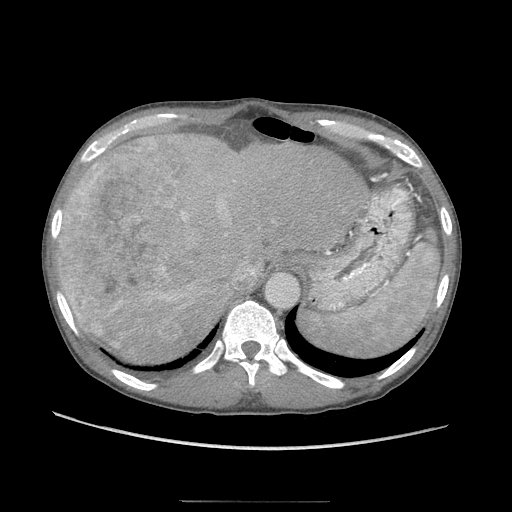
Contrast-enhanced abdominal CT (liver protocol), one axial slice; position 73 of 103 along the scan axis; reconstruction kernel STANDARD; 120 kVp; soft-tissue window (W 400 / L 40 HU); 2.5 mm slice thickness; 512 × 512 image matrix, field of view 380 × 380 mm. From the clinical record (not read from this slice): diagnosis: hepatocellular carcinoma (patient treated with transarterial chemoembolisation; whether this scan precedes or follows treatment is not stated here); TNM stage (as recorded): Stage-IIIA; Child-Pugh class: A; tumour size: 16 cm.
Structures marked on this image (semi-automatically segmented with operator editing):
- liver parenchyma outside the tumour (the mass and vessels are separate outlines, so this box may not span the whole liver): bounding box (x1, y1, x2, y2) in pixels: (56, 134, 366, 362)
- mass: (59, 148, 184, 339)
- liver vessels: (101, 150, 204, 301)